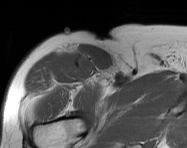
MRI of an extremity soft-tissue mass, one axial slice; slice 112 of 114 in the series (ordered by position); MR volume resampled by the dataset authors to the PET/CT grid (not the native acquisition matrix); 3.27 mm slice thickness; 187 × 148 image matrix, field of view 183 × 145 mm. Male patient. Case-level facts recorded for this patient, not image findings: histological type: pleiomorphic leiomyosarcoma; grade: intermediate; site of the primary tumour: right thigh.
Annotated regions visible in this slice (expert contour drawn on MRI and transferred to this co-registered scan by the dataset authors):
- gross tumour volume including surrounding oedema: bounding box <73,54,94,76> (left, top, right, bottom; pixels)